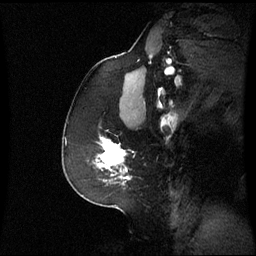
Breast MRI (dynamic contrast-enhanced), one sagittal slice; slice 41 of 60 in the series (ordered by position); dynamic contrast-enhanced series, image 2 of 3 at this slice position (ordered by acquisition); 1.5 T; TE 4.2 ms, TR 8.9 ms; 256 × 256 image matrix, field of view 230 × 230 mm. Female patient, age 59 years. From the clinical record (not read from this slice): setting: breast cancer imaged before/during neoadjuvant chemotherapy; receptor status: triple-negative.
Structures marked on this image (semi-automatically segmented with operator editing):
- analysis volume of interest (the breast-tissue region the enhancement analysis was run in; not a lesion): bounding box [x1, y1, x2, y2] px = [88, 137, 131, 183]
- tumour enhancement mask (voxels above the 70 % enhancement threshold inside the analysis volume of interest): [99, 137, 130, 179]